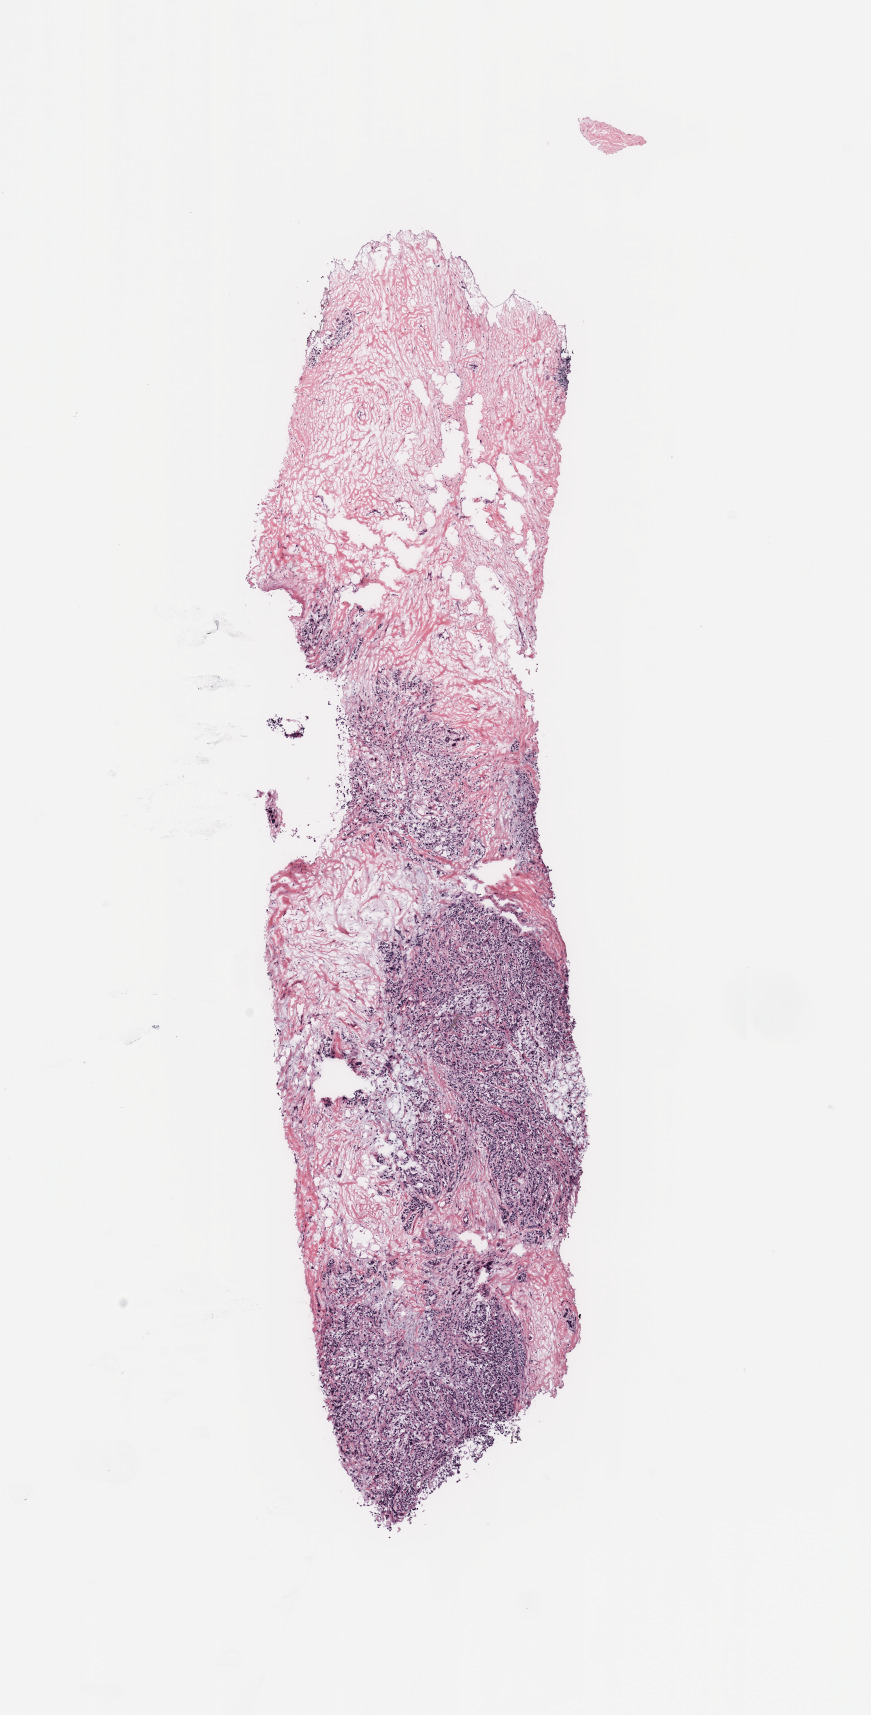
Hematoxylin and eosin (H&E) stained whole-slide image, a low-resolution overview of the entire scanned area, about 6.9 x 13.6 mm (slide scanned at 20x); breast, tissue type not recorded. 71-year-old patient.
Patient diagnosis: Invasive lobular carcinoma.